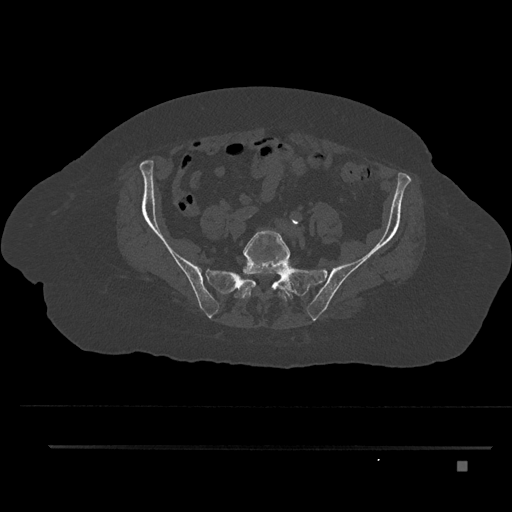
CT including the spine, one axial slice. Position 19 of 797 along the scan axis. 120 kVp. Bone window (W 1800 / L 400 HU). 0.5 mm slice thickness. 512 × 512 image matrix. Patient: female, 76 years. Case-level facts recorded for this patient, not image findings: primary cancer: lung; vertebrae with lytic lesions (as recorded): T11, L3.
Structures marked on this image (semi-automatic segmentation, software-assisted and operator-edited):
- L5 vertebra: bounding box <242,230,290,301> (left, top, right, bottom; pixels)